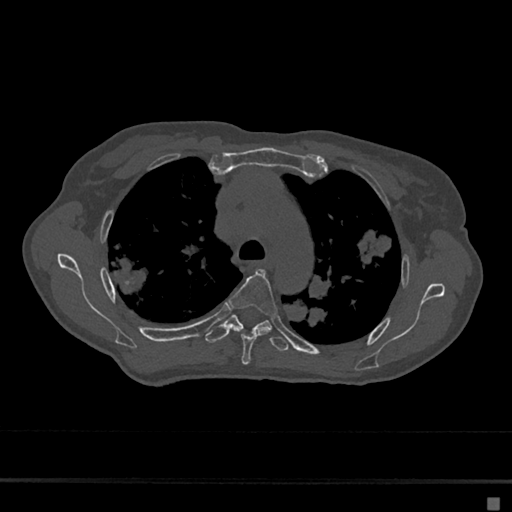
CT including the spine, one axial slice. Position 486 of 797 along the scan axis. 120 kVp. Bone window (W 1800 / L 400 HU). 512 × 512 image matrix, field of view 360 × 360 mm. Female patient, age 68 years. Case-level facts recorded for this patient, not image findings: primary cancer: renal.
Annotated regions visible in this slice (semi-automatically segmented with operator editing):
- T4 vertebra: bounding box (x1, y1, x2, y2) in pixels: (228, 268, 277, 365)
- T5 vertebra: (205, 312, 288, 352)